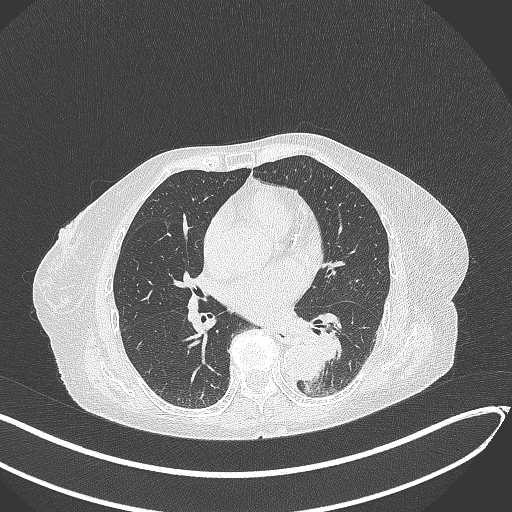
Chest CT, one axial slice. Slice 118 of 324 in the series (ordered by position). Reconstruction kernel B70f. Lung window (W 1500 / L -600 HU). 512 × 512 image matrix, field of view 400 × 400 mm. Female patient, age 82 years. Case-level facts recorded for this patient, not image findings: clinical TNM (as recorded): T1b N0 M1.
Annotated regions visible in this slice (rectangle marked by the reading radiologist):
- lung tumour (recorded histology: adenocarcinoma): bounding box (x1, y1, x2, y2) in pixels: (298, 328, 346, 368)